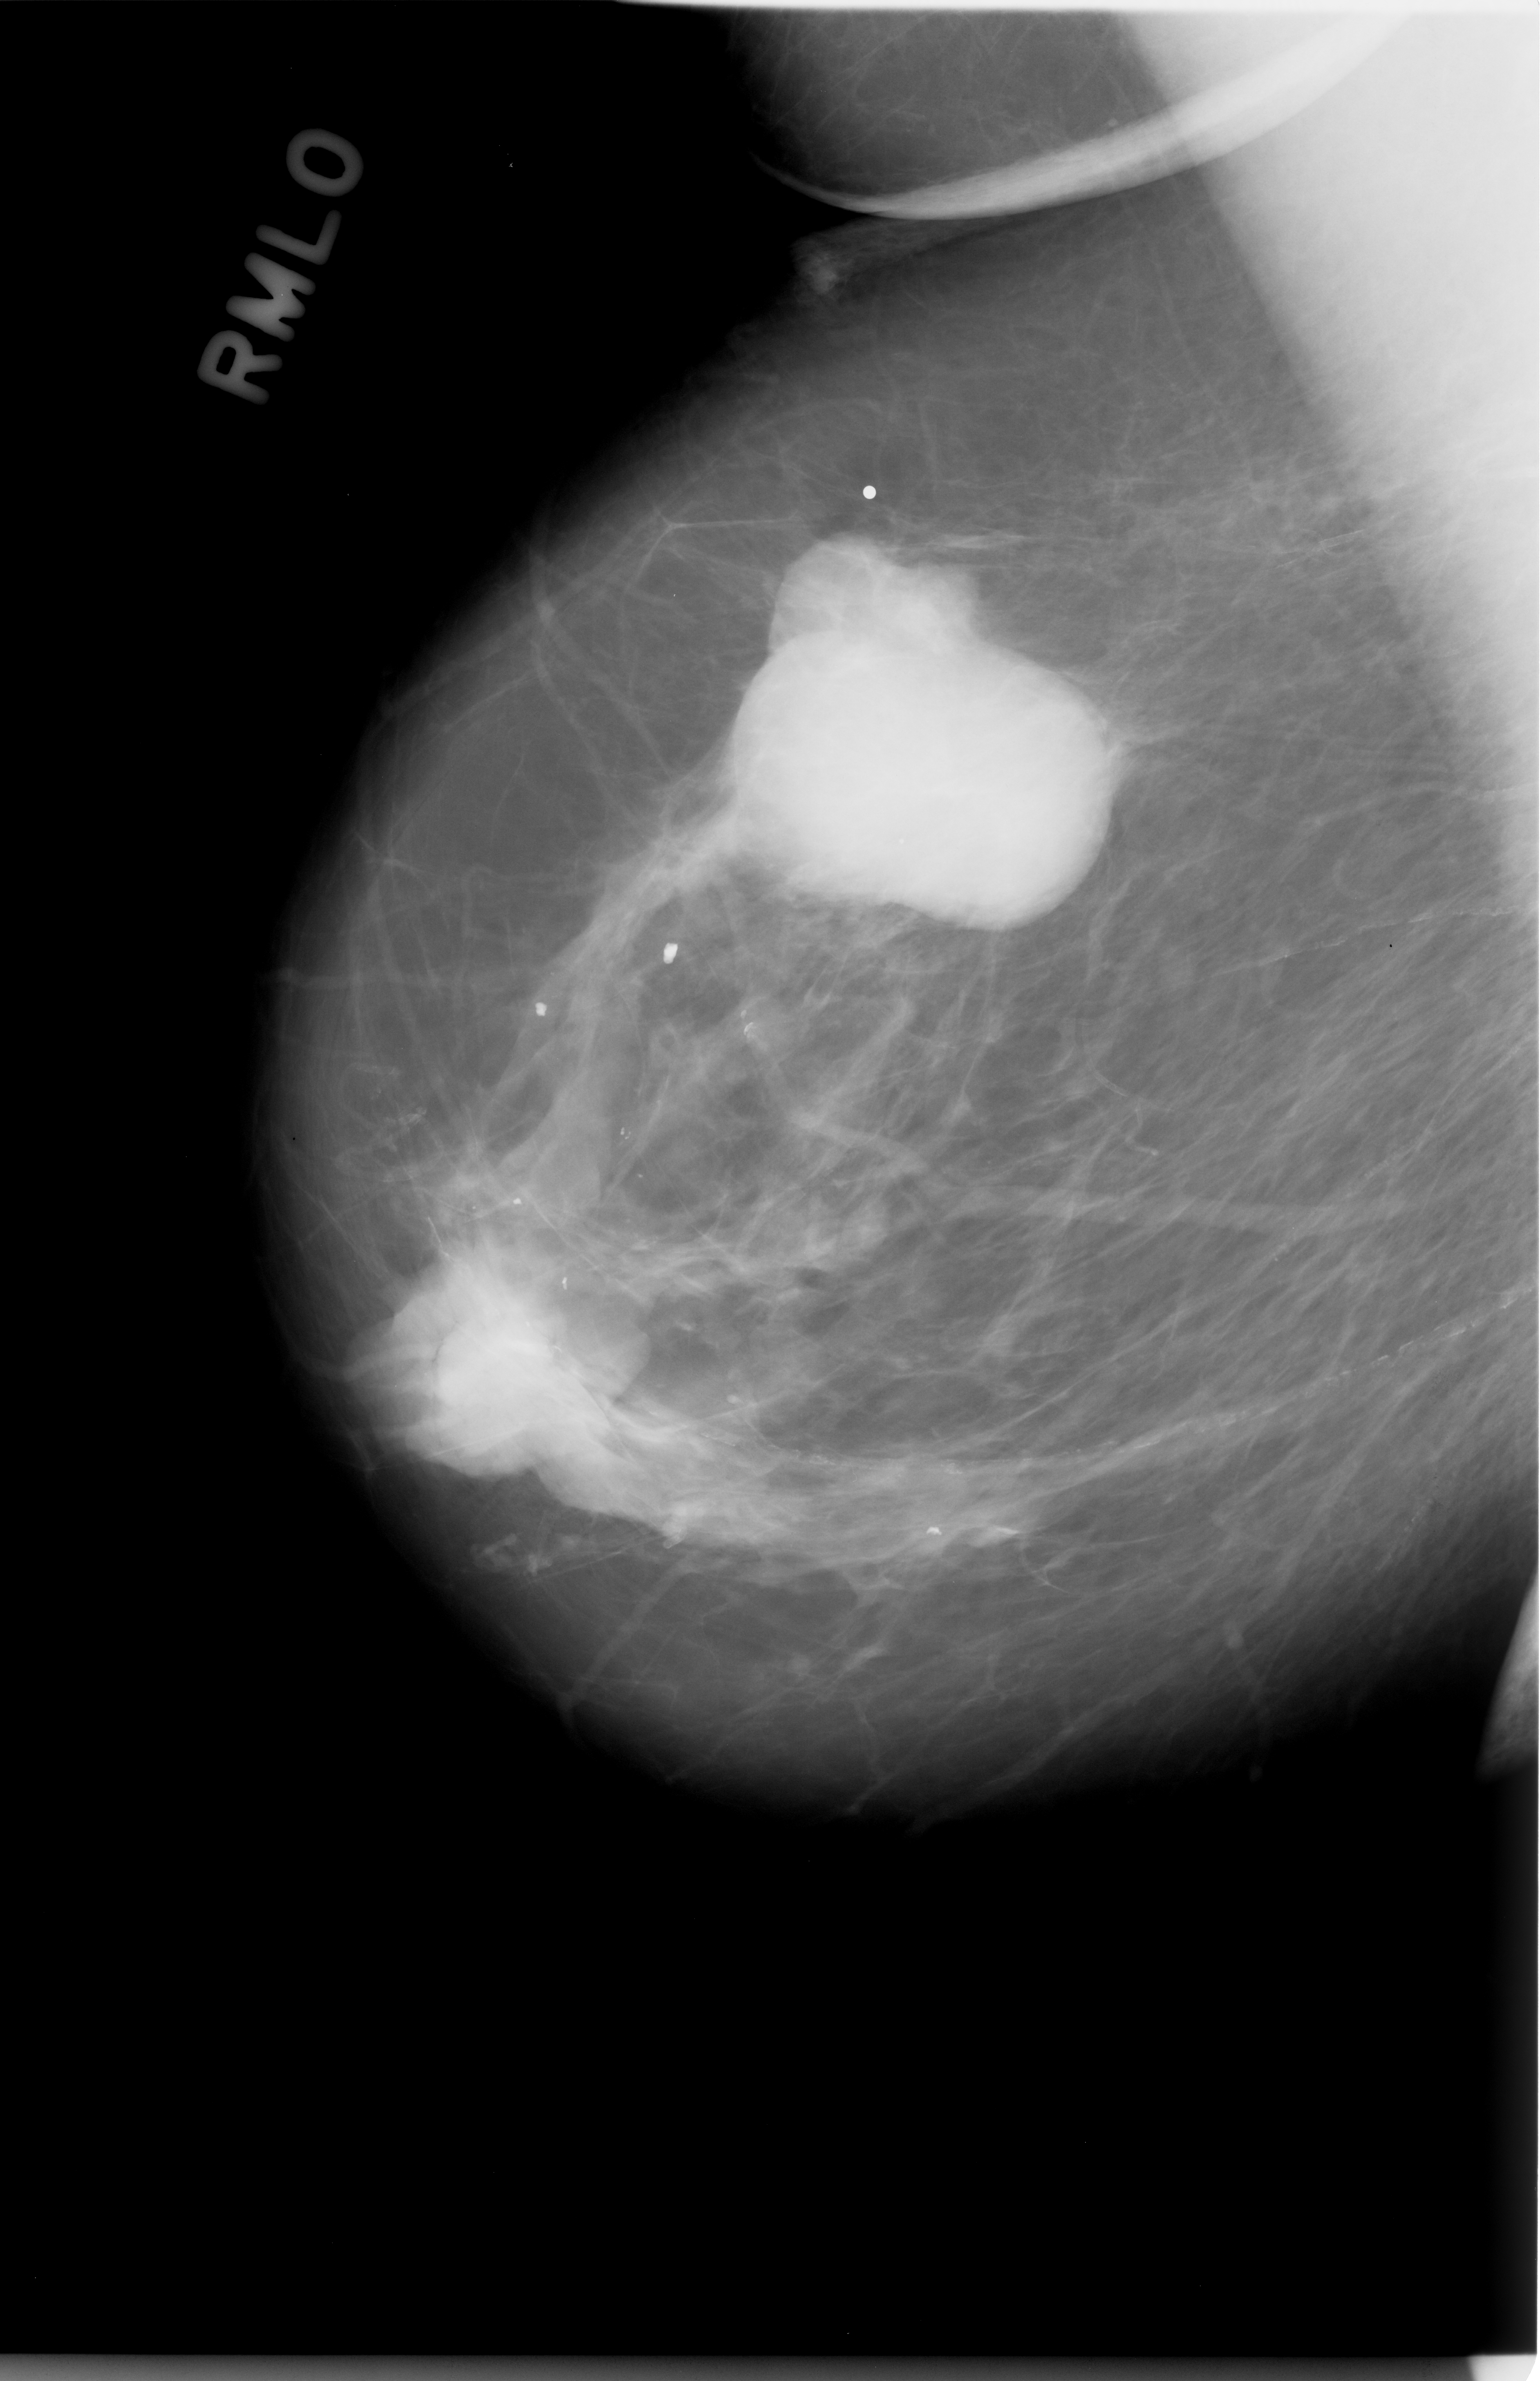
Scanned film-screen mammogram; right breast; mediolateral oblique (MLO) view; breast composition: almost entirely fatty (BI-RADS density category 1 of 4).
Marked findings (only marked abnormalities are described; nothing is implied about the rest of the image): Finding 1 of 2: mass, shape lobulated, margins circumscribed; BI-RADS assessment category 5; subtlety rating 5 on a 1 (subtle) to 5 (obvious) scale; pathology (as recorded): malignant. Finding 2 of 2: mass, shape lobulated, margins circumscribed; BI-RADS assessment category 5; pathology (as recorded): malignant.